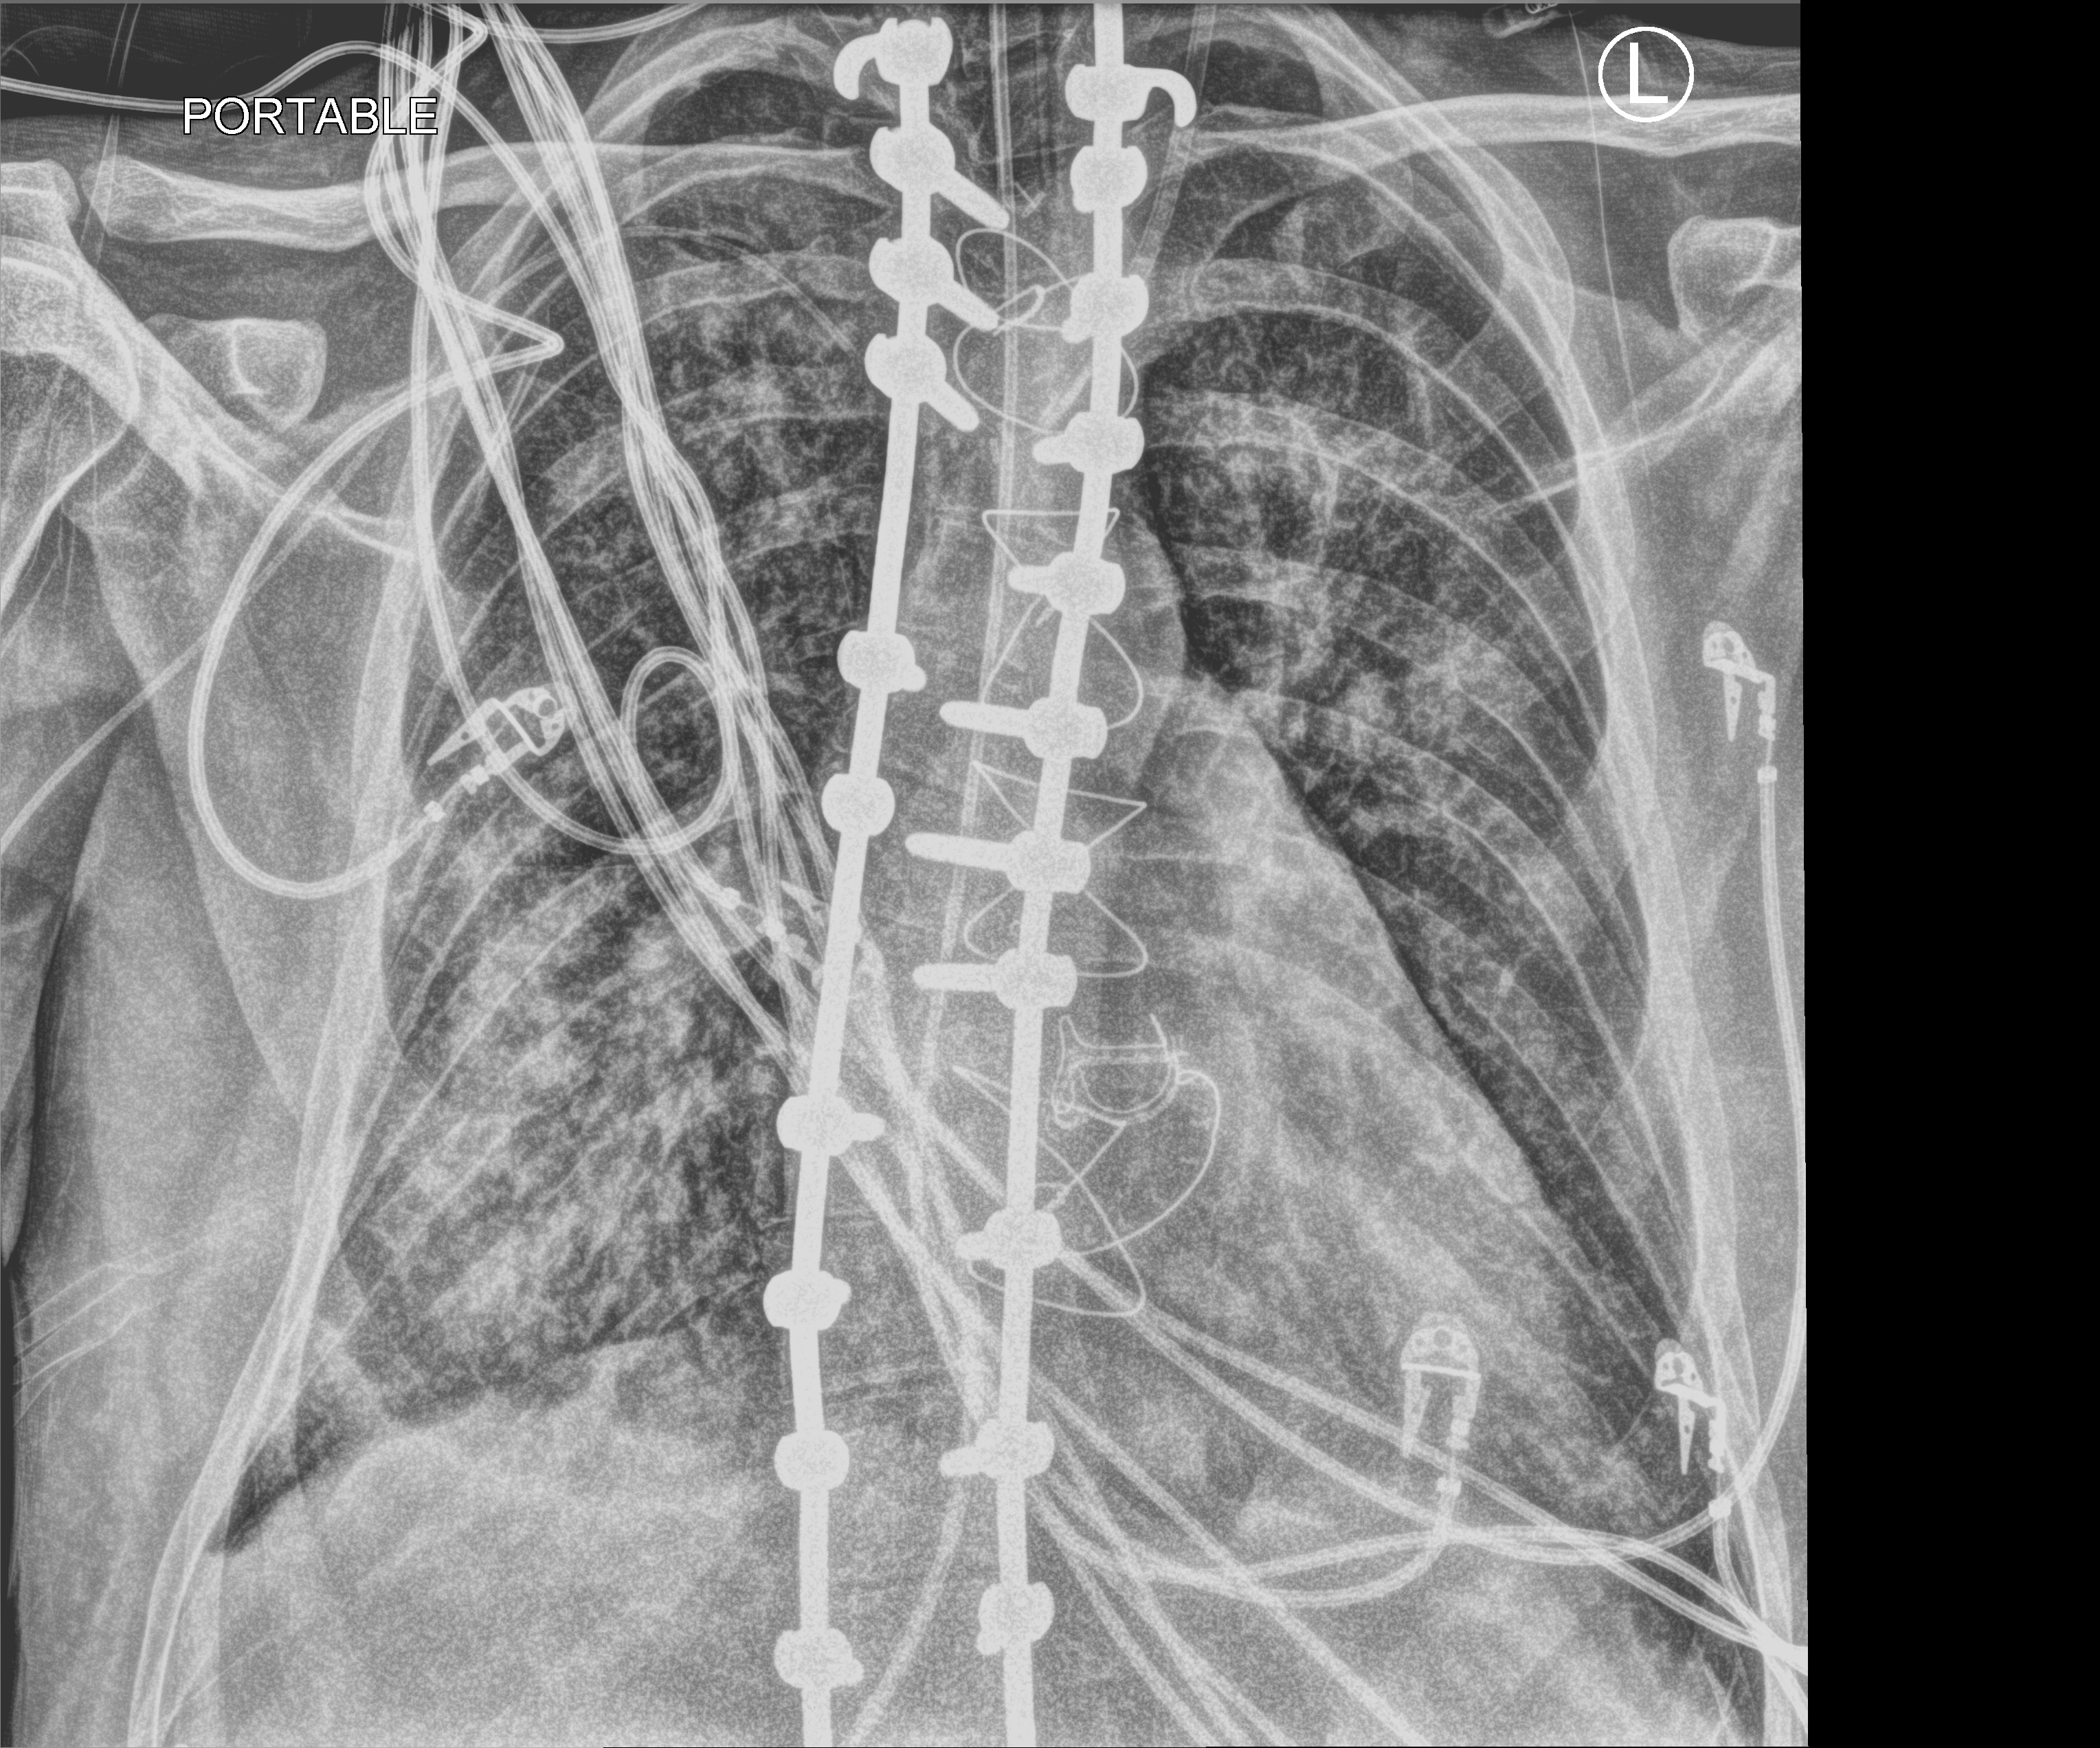
Chest X-ray (portable), anteroposterior (AP) projection. Patient hospitalised with COVID-19, aged 18–59 years.
Admission-level facts for this patient (not findings on this image; timing relative to this image not recorded):
- mechanically ventilated during this hospital stay: yes